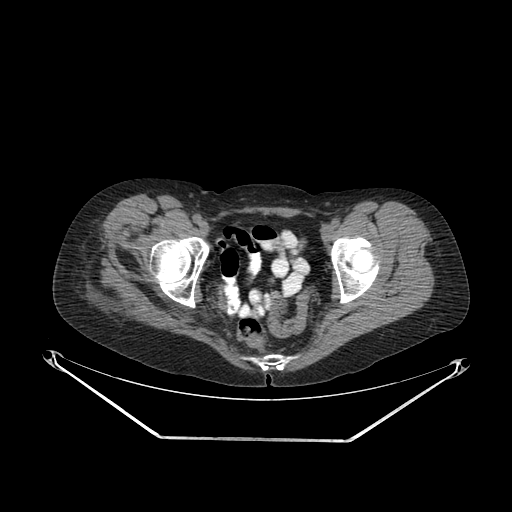
CT of an extremity soft-tissue mass (from a PET/CT study), one axial slice. Slice 53 of 267 in the series (ordered by position). 140 kVp. Soft-tissue window (W 400 / L 40 HU). 3.75 mm slice thickness. 512 × 512 image matrix. Female patient. Case-level facts recorded for this patient, not image findings: histological type: epithelioid sarcoma with vascular differentiation; site of the primary tumour: right buttock.
Annotated regions visible in this slice (expert contour drawn on MRI and transferred to this co-registered scan by the dataset authors):
- gross tumour volume (mass): bounding box (x1, y1, x2, y2) in pixels: (78, 267, 138, 320)